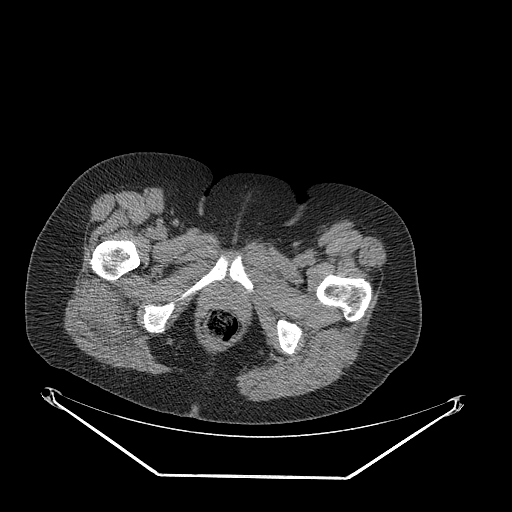
CT of an extremity soft-tissue mass (from a PET/CT study), one axial slice; position 59 of 257 along the scan axis; reconstruction kernel STANDARD; soft-tissue window (W 400 / L 40 HU); 512 × 512 image matrix, field of view 500 × 500 mm. Female patient. From the clinical record (not read from this slice): histological type: synovial sarcoma; grade: intermediate; site of the primary tumour: right buttock.
Structures marked on this image (expert contour drawn on MRI and transferred to this co-registered scan by the dataset authors):
- gross tumour volume including surrounding oedema: bounding box [x1, y1, x2, y2] px = [84, 285, 156, 346]
- gross tumour volume (mass): [85, 285, 131, 320]